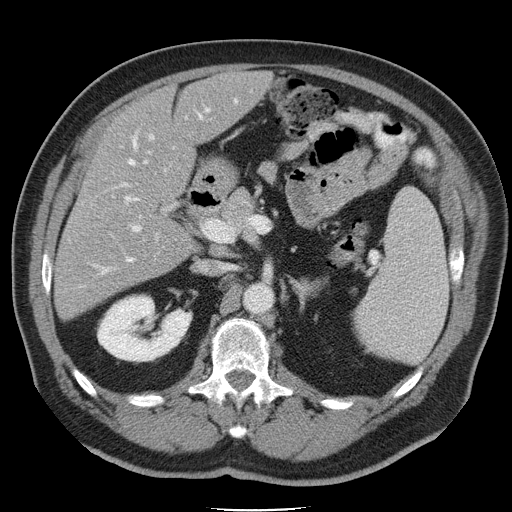
Contrast-enhanced abdominal CT, one axial slice; position 23 of 45 along the scan axis; 120 kVp; intravenous contrast given; soft-tissue window (W 400 / L 40 HU); 512 × 512 image matrix. Male patient, age 65 years. Case-level facts recorded for this patient, not image findings: diagnosis: colorectal cancer liver metastases, imaged before liver resection; multiple liver metastases: yes; largest metastasis: 4.9 cm; disease in both lobes: no.
Annotated regions visible in this slice (manually delineated by an expert):
- hepatic veins: bounding box (x1, y1, x2, y2) in pixels: (92, 98, 238, 275)
- liver: (55, 72, 269, 318)
- planned liver remnant (the part of the liver to remain after resection): (100, 72, 269, 196)
- portal vein (with intrahepatic branches): (124, 135, 159, 242)